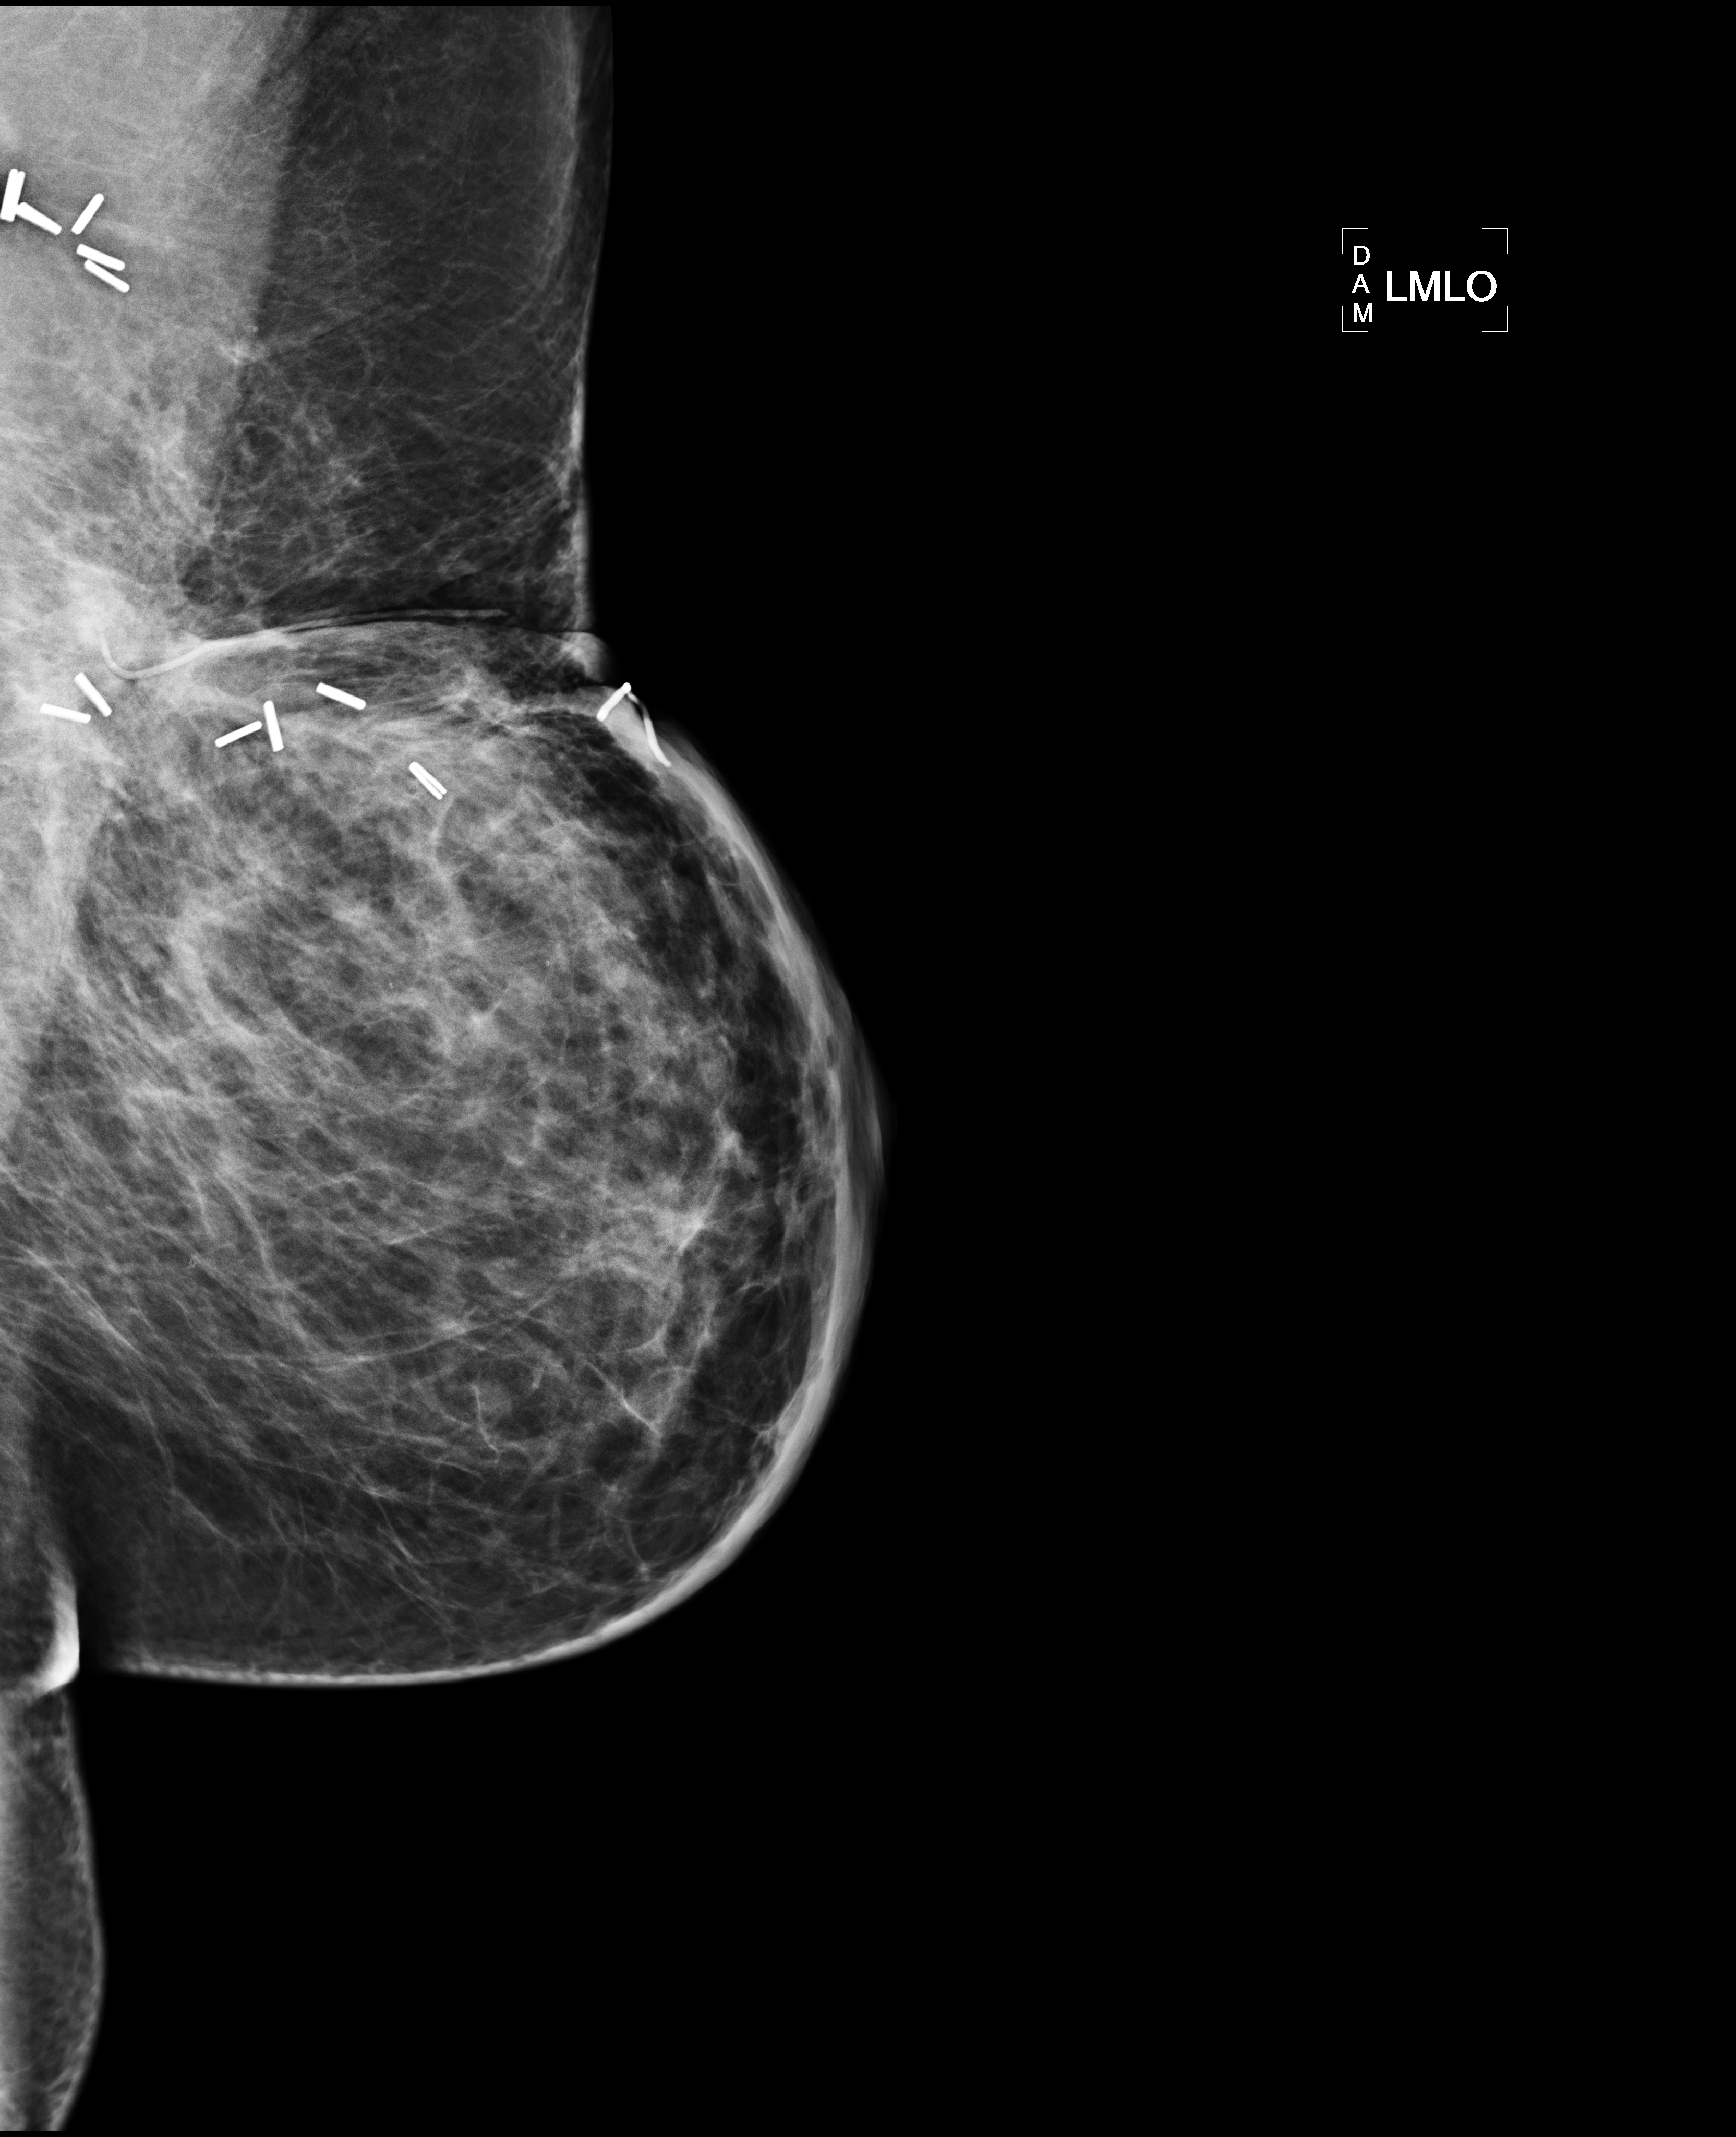
Mammogram, left breast, MLO view; patient in her 50s.
Pathology recorded for this patient (not read from this image): pathology diagnosis: Invasive ductal CA (left breast); receptor status (as recorded): ER pos, PR pos (weak), HER2 neg; pathology report notes: re-bx [date] was scar tissue from RT rx.